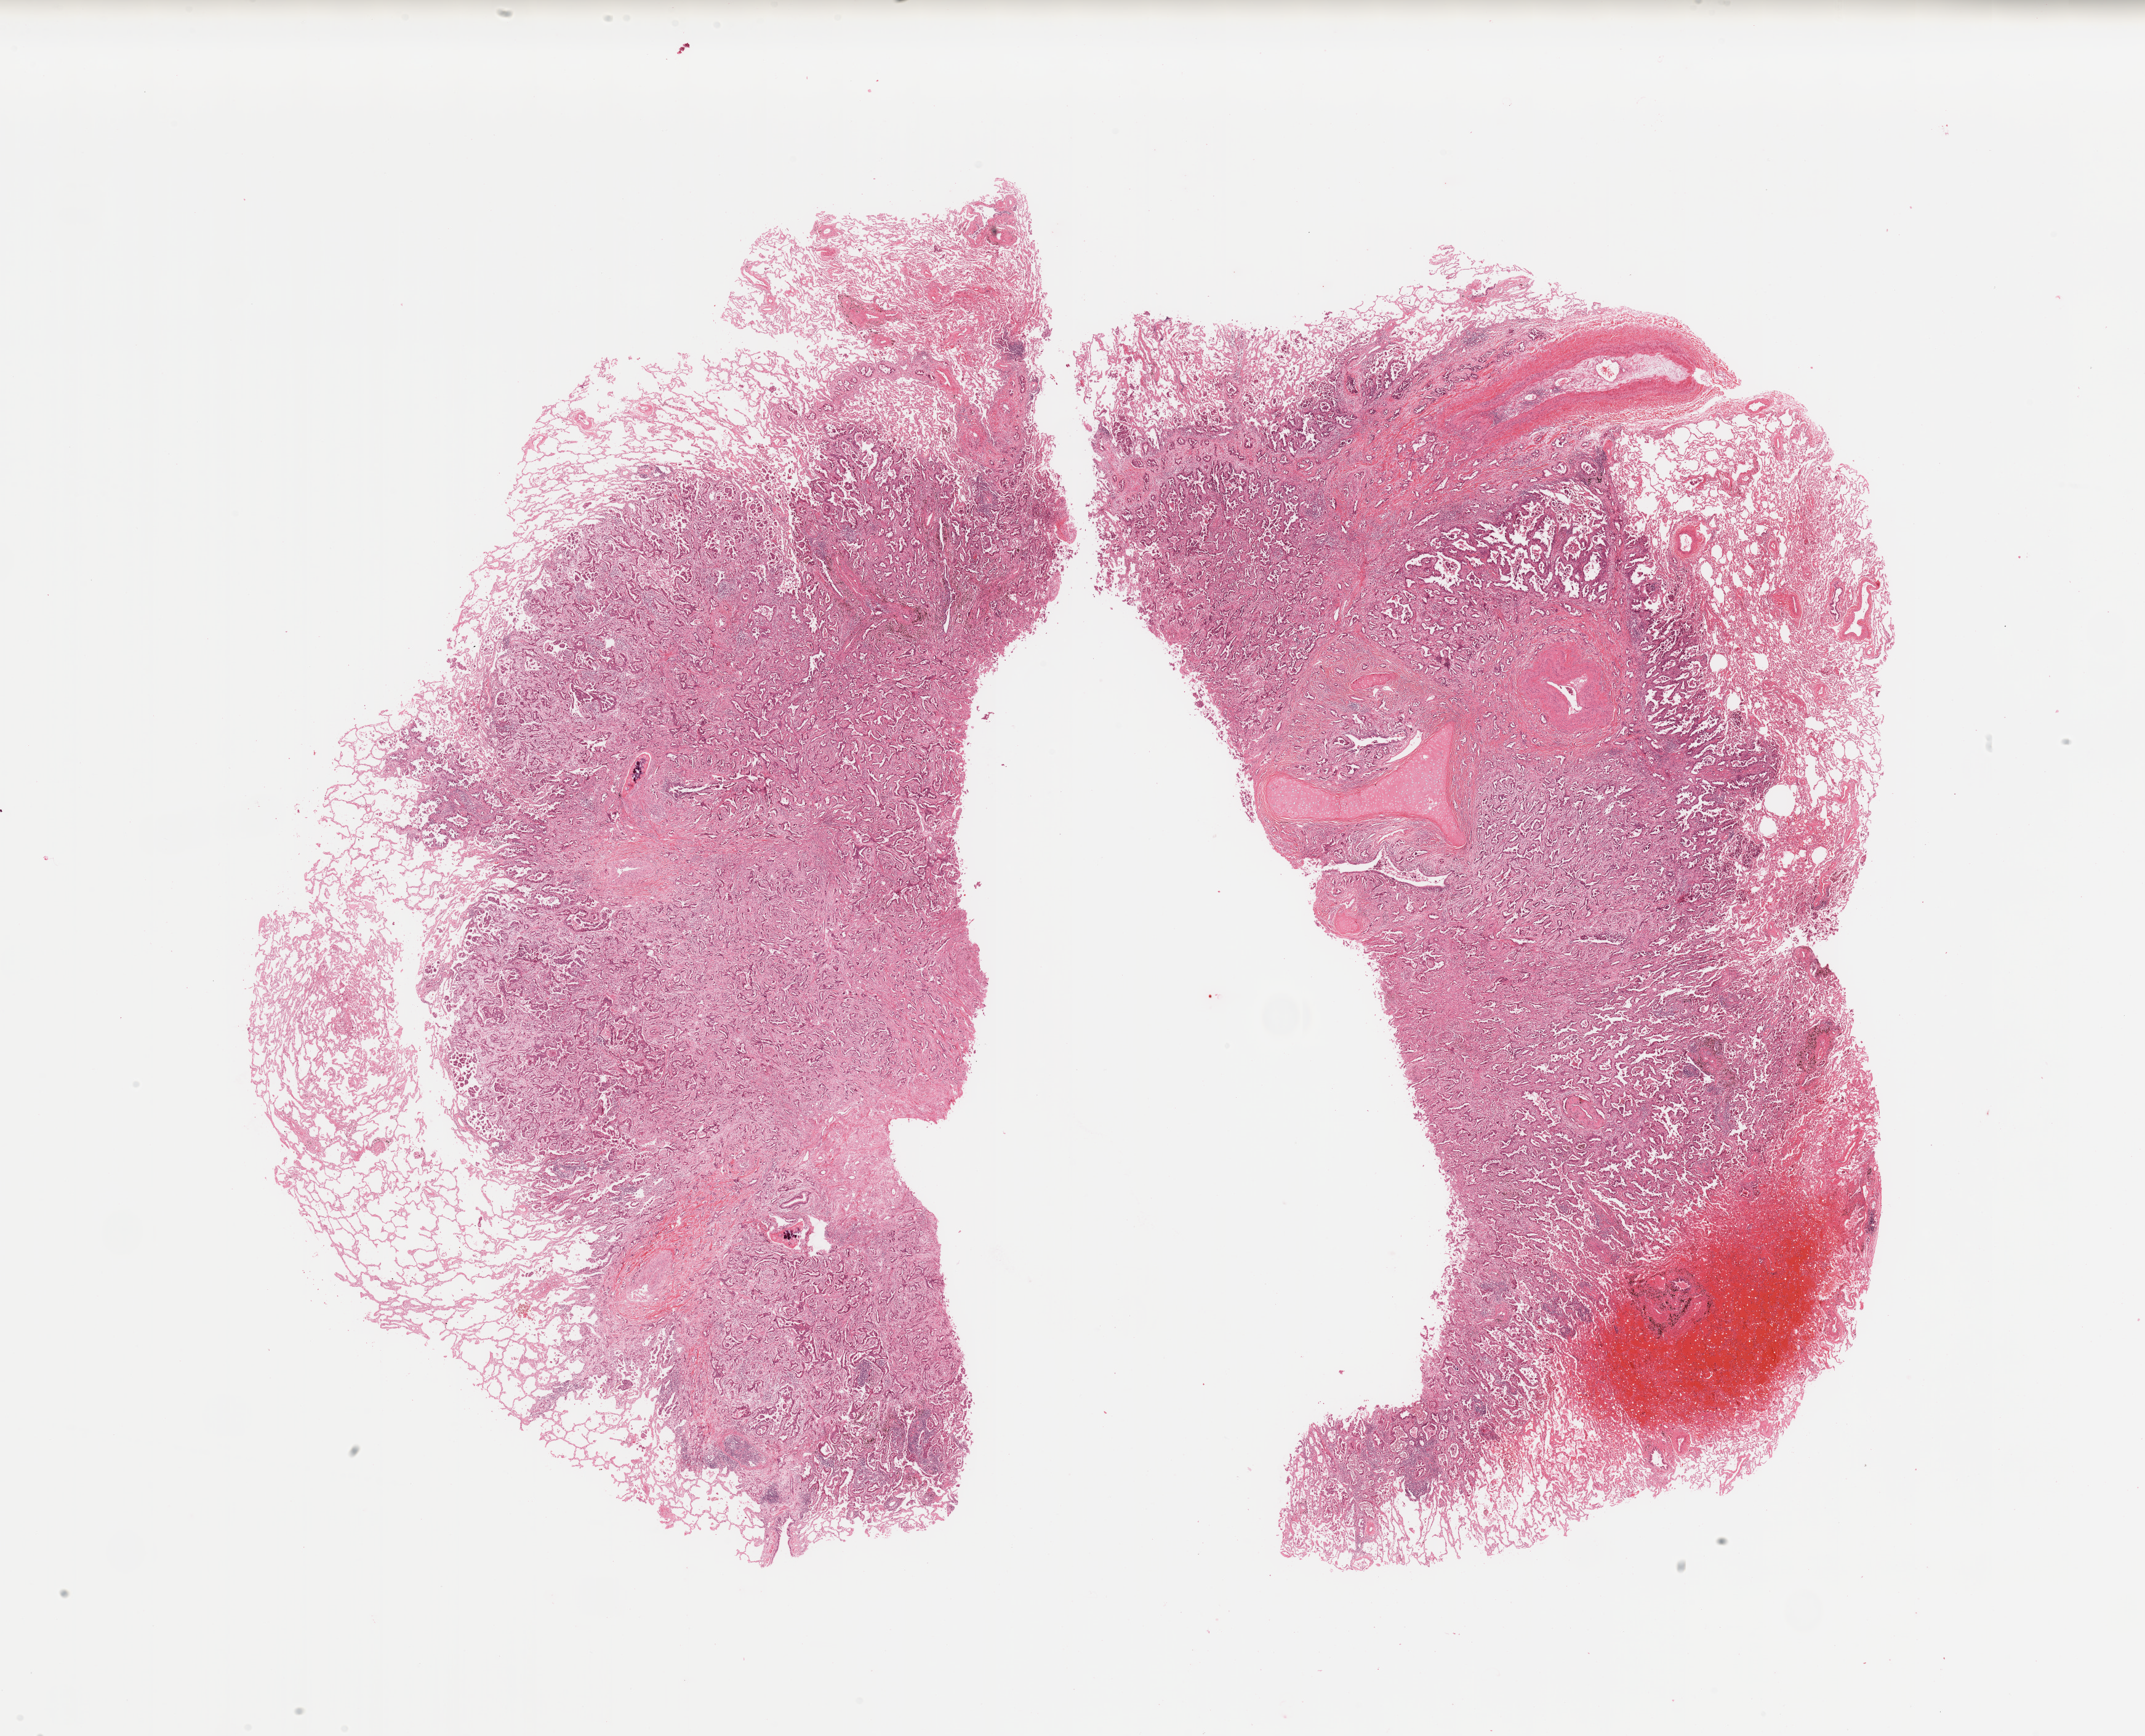
H&E-stained whole-slide image, low-resolution overview of the scanned area, about 27.6 x 22.3 mm (acquisition: 20x scan); tumour tissue sample, lung. Patient: female, age 65 years. Histologic grade: G3 (poorly differentiated).
Histologic diagnosis: Adenocarcinoma, NOS. AJCC pathologic stage: IB.